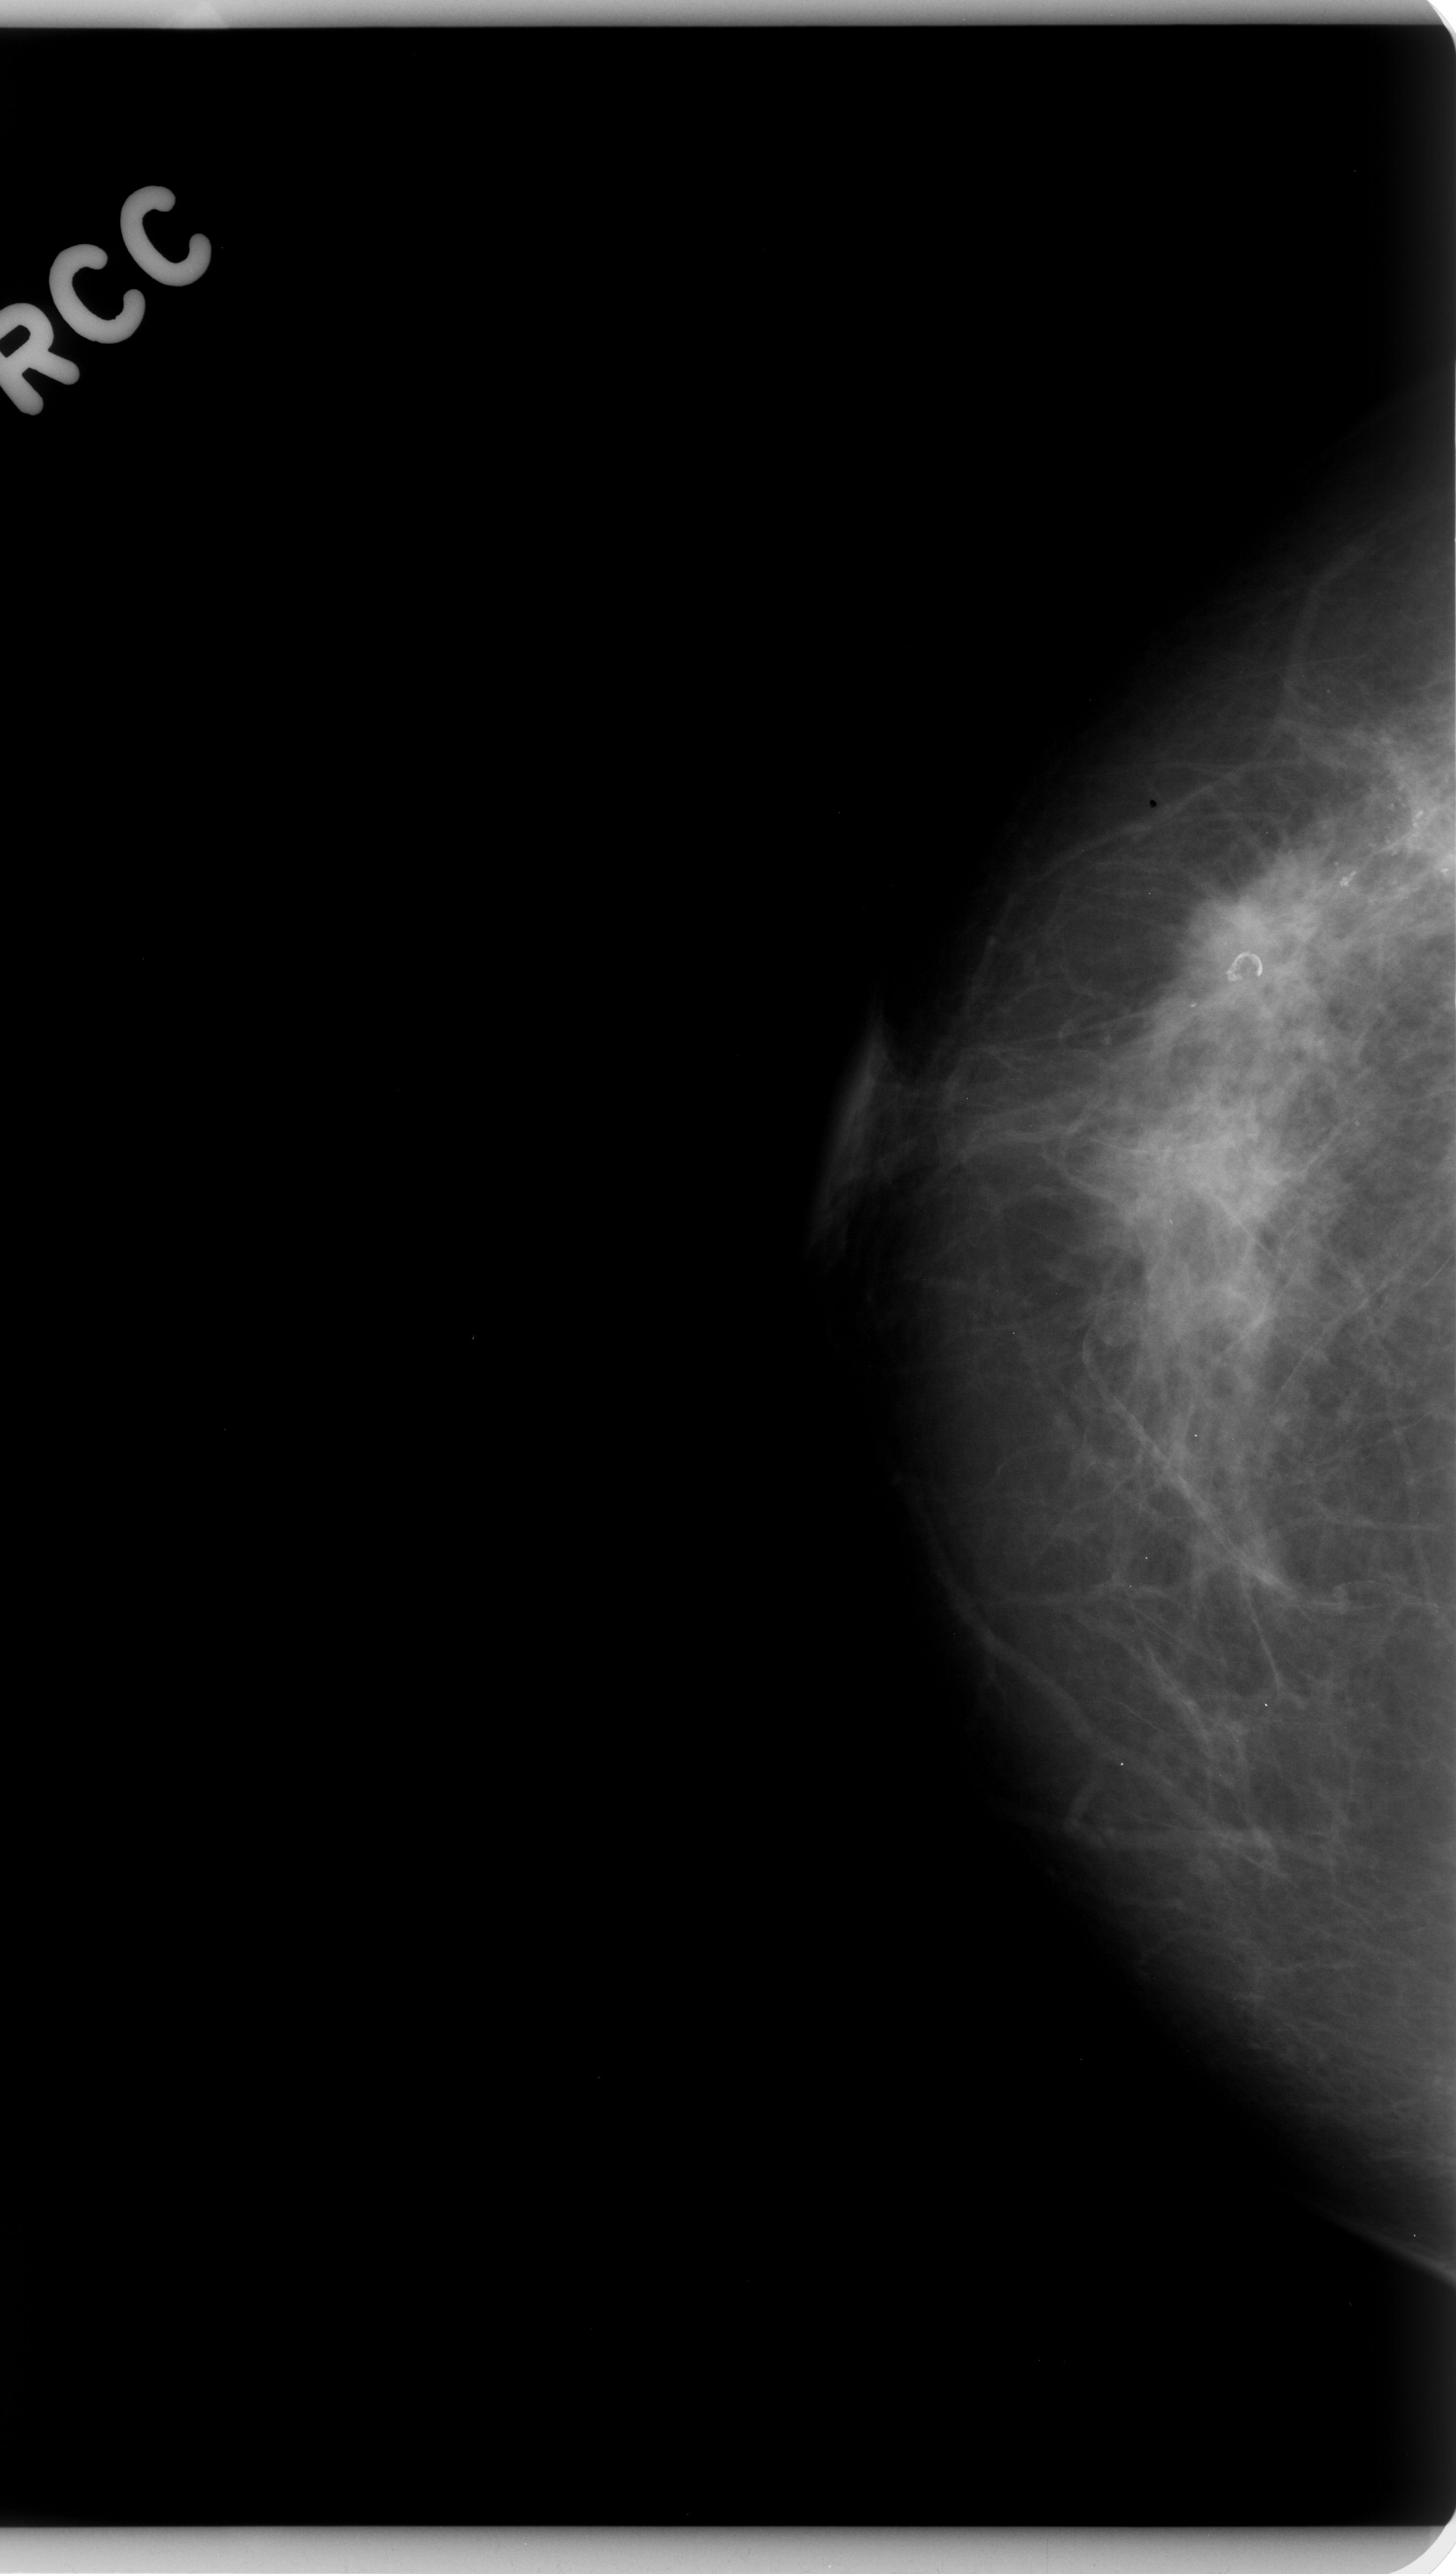
Scanned film-screen mammogram, right breast, CC view.
Marked findings (only marked abnormalities are described; nothing is implied about the rest of the image): calcifications, morphology pleomorphic, distribution segmental; BI-RADS assessment category 5; subtlety rating 5 on a 1 (subtle) to 5 (obvious) scale; pathology result (as recorded, not read from the image): malignant.